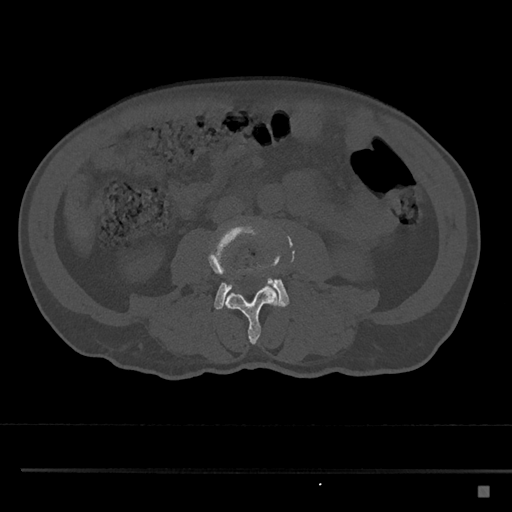
CT including the spine, one axial slice. Position 671 of 797 along the scan axis. 120 kVp. Bone window (W 1800 / L 400 HU). 0.5 mm slice thickness. 512 × 512 image matrix, field of view 391 × 391 mm. Patient: male, 59 years. From the clinical record (not read from this slice): primary cancer: prostate.
Annotated regions visible in this slice (semi-automatically segmented with operator editing):
- L3 vertebra: bounding box (x1, y1, x2, y2) in pixels: (208, 222, 280, 345)
- L4 vertebra: (214, 254, 290, 310)